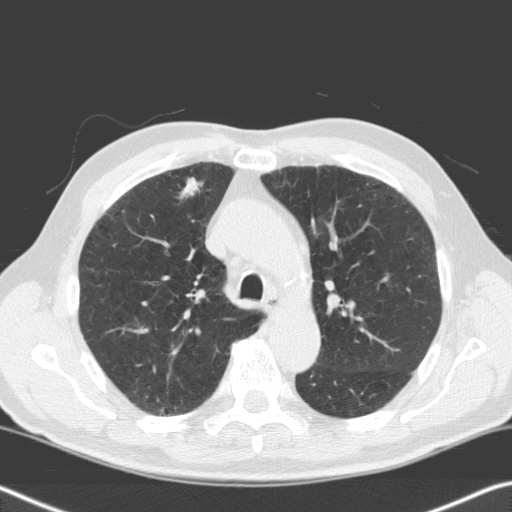
Low-dose screening chest CT, one axial slice. 120 kVp. Lung window (W 1500 / L -600 HU). 3.2 mm slice thickness. 512 × 512 image matrix, field of view 343 × 343 mm.
Structures marked on this image (outlined manually by an expert reader):
- lesion 1 (tumor, upper lobe of right lung): box from (x=180, y=177) to (x=203, y=199) px